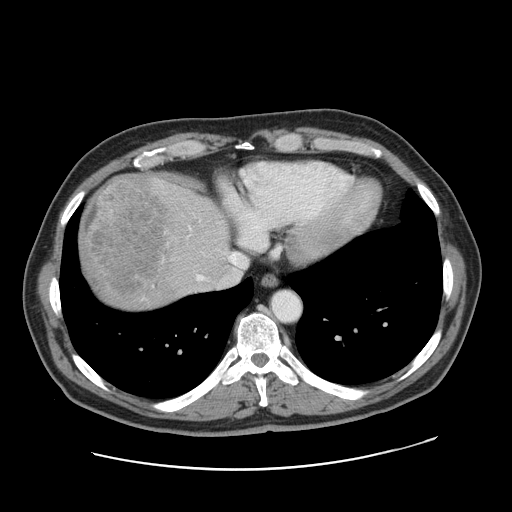
Contrast-enhanced abdominal CT, one axial slice. Position 145 of 178 along the scan axis. 120 kVp. Soft-tissue window (W 400 / L 40 HU). 2.5 mm slice thickness. 512 × 512 image matrix, field of view 403 × 403 mm. Male patient, age 63 years. From the clinical record (not read from this slice): diagnosis: colorectal cancer liver metastases, imaged before liver resection; multiple liver metastases: yes; largest metastasis: 8 cm; disease in both lobes: yes.
Outlined on this slice (manually delineated by an expert):
- hepatic veins: bounding box <197,252,247,280> (left, top, right, bottom; pixels)
- liver: <79,174,230,311>
- planned liver remnant (the part of the liver to remain after resection): <183,190,230,263>
- liver metastasis: <82,175,166,294>